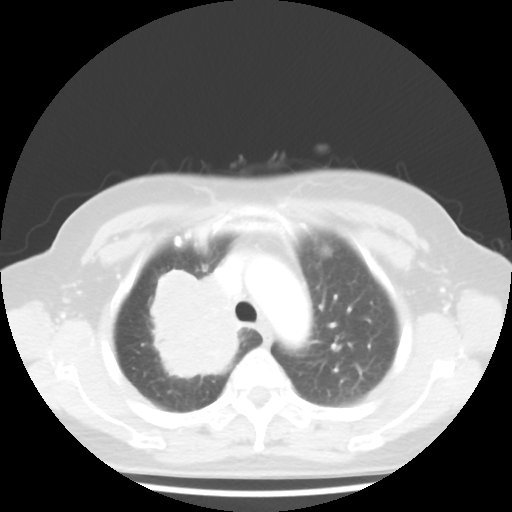
Chest CT, one axial slice. Position 34 of 44 along the scan axis. 100 kVp. Lung window (W 1500 / L -600 HU). 5 mm slice thickness. 512 × 512 image matrix, field of view 316 × 316 mm. Patient: female, 62 years. From the clinical record (not read from this slice): clinical TNM (as recorded): T3 N0 M0.
Structures marked on this image (bounding box drawn by a radiologist):
- lung tumour (recorded histology: small cell carcinoma): bounding box <132,250,249,392> (left, top, right, bottom; pixels)